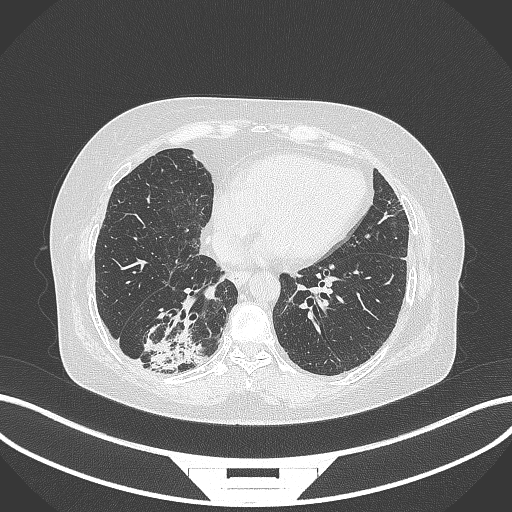
Chest CT, one axial slice. Slice 76 of 296 in the series (ordered by position). Reconstruction kernel B70f. 120 kVp. Lung window (W 1500 / L -600 HU). 512 × 512 image matrix, field of view 400 × 400 mm. Patient: female, 65 years. From the clinical record (not read from this slice): clinical TNM (as recorded): T2b N1 M0; histopathological grade: G1.
Outlined on this slice (rectangle marked by the reading radiologist):
- lung tumour (recorded histology: adenocarcinoma): bounding box (x1, y1, x2, y2) in pixels: (140, 322, 210, 374)